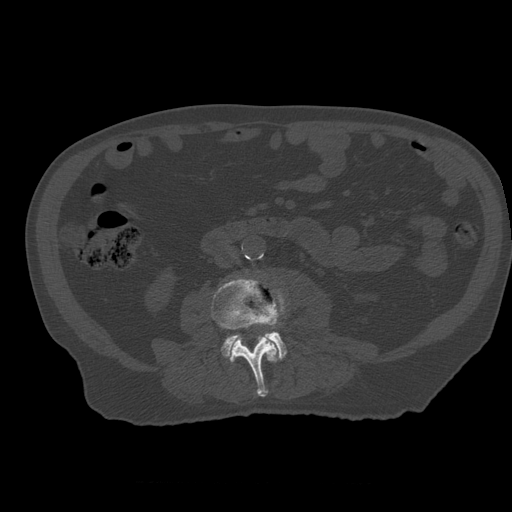
CT including the spine, one axial slice; slice 181 of 399 in the series (ordered by position); reconstruction kernel STANDARD; bone window (W 1800 / L 400 HU); 1.25 mm slice thickness; 512 × 512 image matrix, field of view 407 × 407 mm. Patient age 73 years. From the clinical record (not read from this slice): primary cancer: prostate; vertebrae with lytic lesions (as recorded): L2.
Outlined on this slice (semi-automatic segmentation, software-assisted and operator-edited):
- L3 vertebra: bounding box (x1, y1, x2, y2) in pixels: (212, 279, 281, 397)
- L4 vertebra: (221, 292, 287, 359)